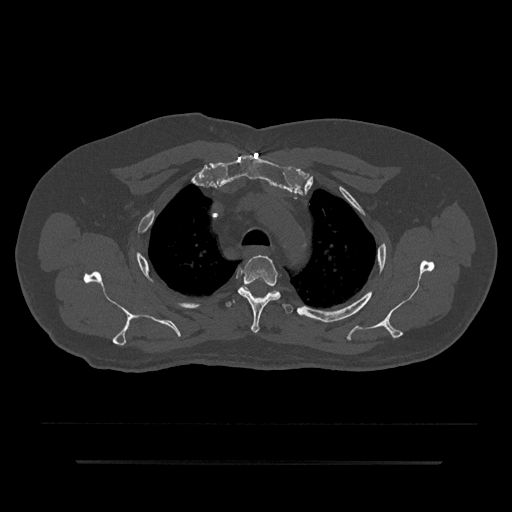
CT including the spine, one axial slice; slice 651 of 797 in the series (ordered by position); reconstruction kernel Br40s/3; bone window (W 1800 / L 400 HU); 0.5 mm slice thickness; 512 × 512 image matrix, field of view 464 × 464 mm. Male patient, age 59 years. From the clinical record (not read from this slice): primary cancer: bile ducts.
Annotated regions visible in this slice (semi-automatic segmentation, software-assisted and operator-edited):
- T3 vertebra: bounding box <238,255,281,333> (left, top, right, bottom; pixels)
- T4 vertebra: <225,292,293,314>